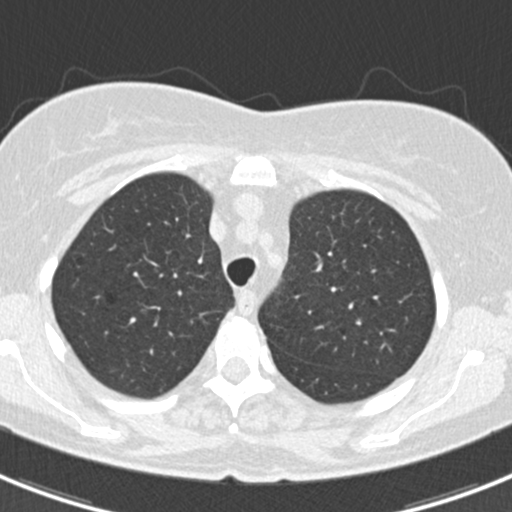
Chest CT (low-dose screening protocol), one axial image. Baseline annual screen. Lung window (W 1500 / L -600 HU). 2 mm slice thickness. Standard (soft-tissue) reconstruction kernel (B30f). 120 kVp. Female participant, aged 60 years at enrolment. Current smoker at enrolment.
• Lesion marked by an expert reader, bounding box (x1, y1, x2, y2) in pixels: (377, 227, 422, 273).
• The screening reader recorded 3 non-calcified nodules or masses ≥4 mm on this exam (lingula, left lower lobe, lingula); which of them this box marks is not recorded.
• Official screen result: positive, change unspecified: nodule(s) >= 4 mm or enlarging nodule(s), mass(es), or other non-specific abnormalities suspicious for lung cancer.
• Later outcome: lung cancer diagnosed 886 days after this screen — non-small cell carcinoma, left upper lobe, poorly differentiated (G3), stage IB (AJCC 6th edition), 7 mm at pathology.